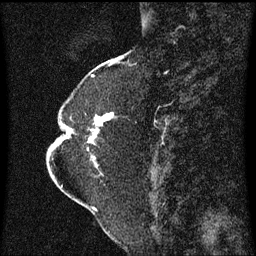
Breast MRI (dynamic contrast-enhanced), one sagittal slice. Slice 23 of 60 in the series (ordered by position). Dynamic contrast-enhanced series, image 2 of 3 at this slice position (ordered by acquisition). 1.5 T. TE 4.2 ms, TR 8.4 ms. 2 mm slice thickness. 256 × 256 image matrix. Patient: female, 52 years. Case-level facts recorded for this patient, not image findings: setting: breast cancer imaged before/during neoadjuvant chemotherapy; receptor status: HR-positive, HER2-negative.
Outlined on this slice (semi-automatic segmentation, software-assisted and operator-edited):
- analysis volume of interest (the breast-tissue region the enhancement analysis was run in; not a lesion): bounding box <64,104,115,167> (left, top, right, bottom; pixels)
- tumour enhancement mask (voxels above the 70 % enhancement threshold inside the analysis volume of interest): <89,114,113,143>